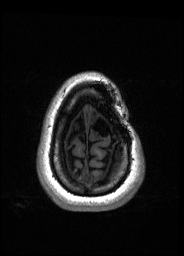
Pre-operative brain MRI before brain-tumour surgery, one axial slice. T1-weighted post-contrast. 1 mm slice thickness. 184 × 256 image matrix, field of view 180 × 250 mm. From the clinical record (not read from this slice): histopathology: Oligodendroglioma; WHO grade: 2; IDH mutation: yes; tumour location: Left Frontal.
Structures marked on this image (expert manual segmentation):
- tumour: bounding box [x1, y1, x2, y2] px = [89, 111, 99, 124]